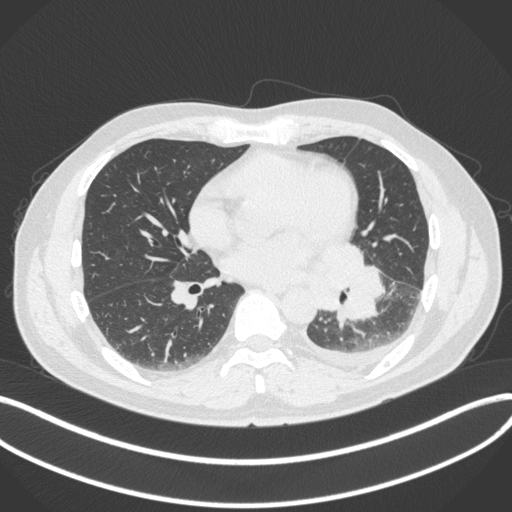
Chest CT, one axial slice; position 163 of 350 along the scan axis; reconstruction kernel B31f; lung window (W 1500 / L -600 HU); 512 × 512 image matrix. Patient: male, 58 years. From the clinical record (not read from this slice): clinical TNM (as recorded): T3 N1 M1b.
Outlined on this slice (bounding box drawn by a radiologist):
- lung tumour (recorded histology: small cell carcinoma): bounding box <313,245,383,325> (left, top, right, bottom; pixels)